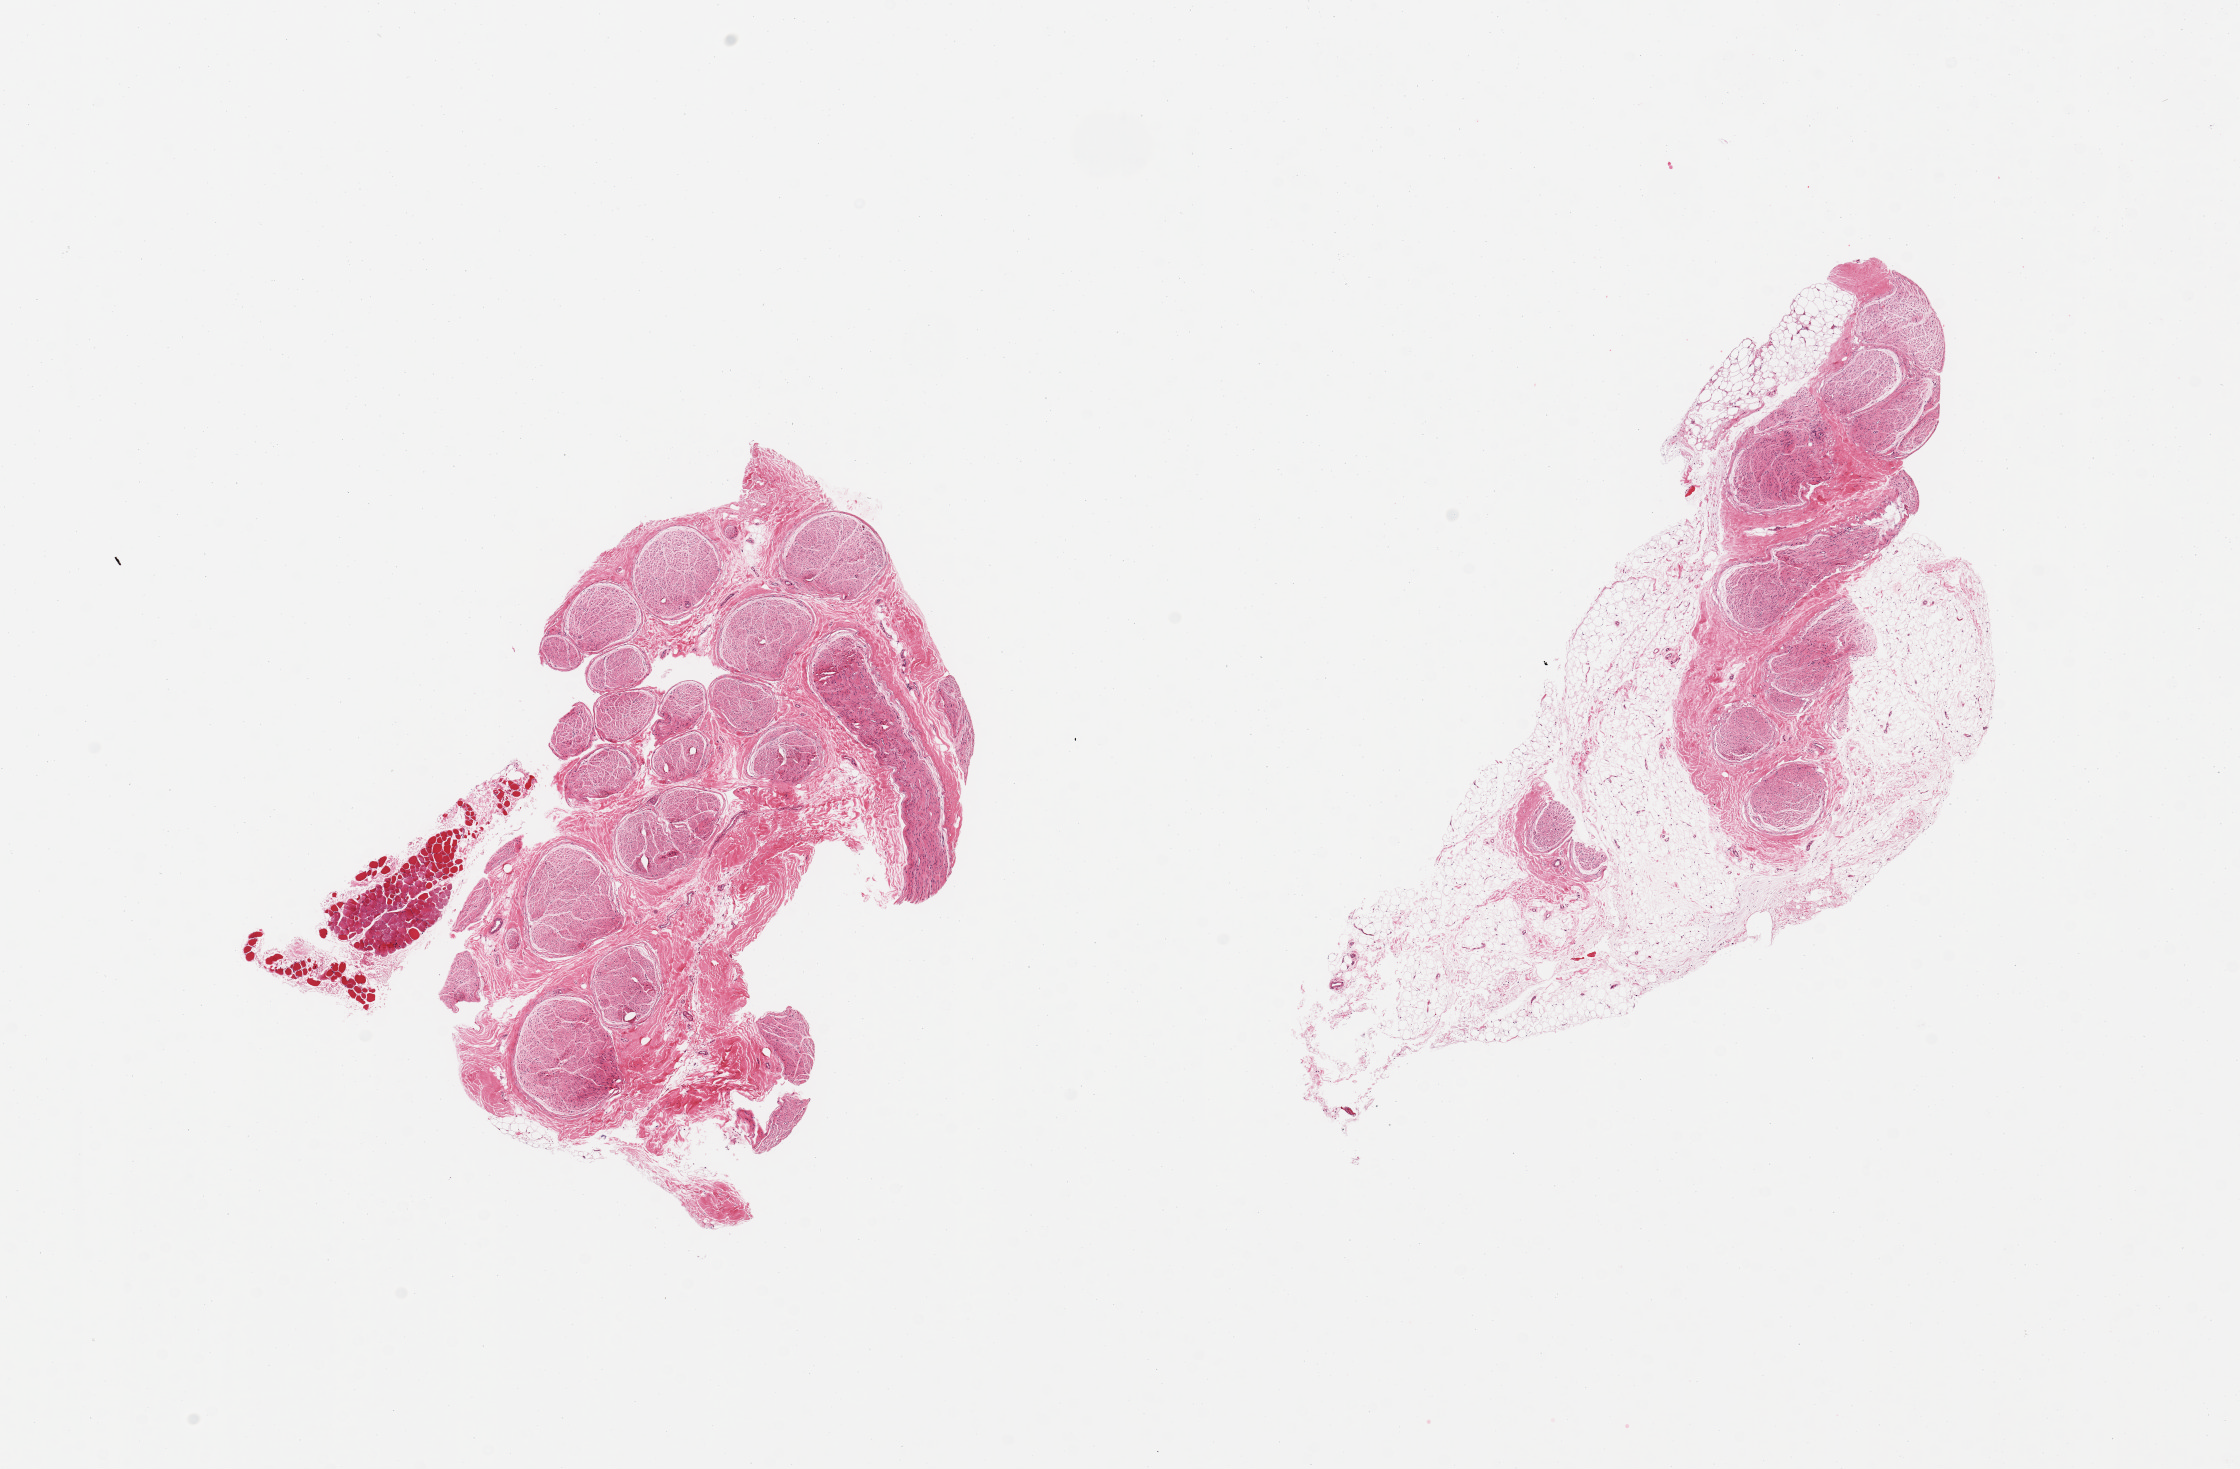
Whole-slide image, haematoxylin and eosin stain — shown as a low-resolution overview of the whole scanned area (about 17.7 x 11.6 mm, from a 20x scan); PAXgene-fixed paraffin-embedded (PFPE) section; target tissue: tibial nerve; donor tissue sample. Donor sex: male.
Reviewer comment on this tissue sample: 2 pieces: 1 with 2.3x0.6mm adherent skeletal muscle; other has 60% external fat content.